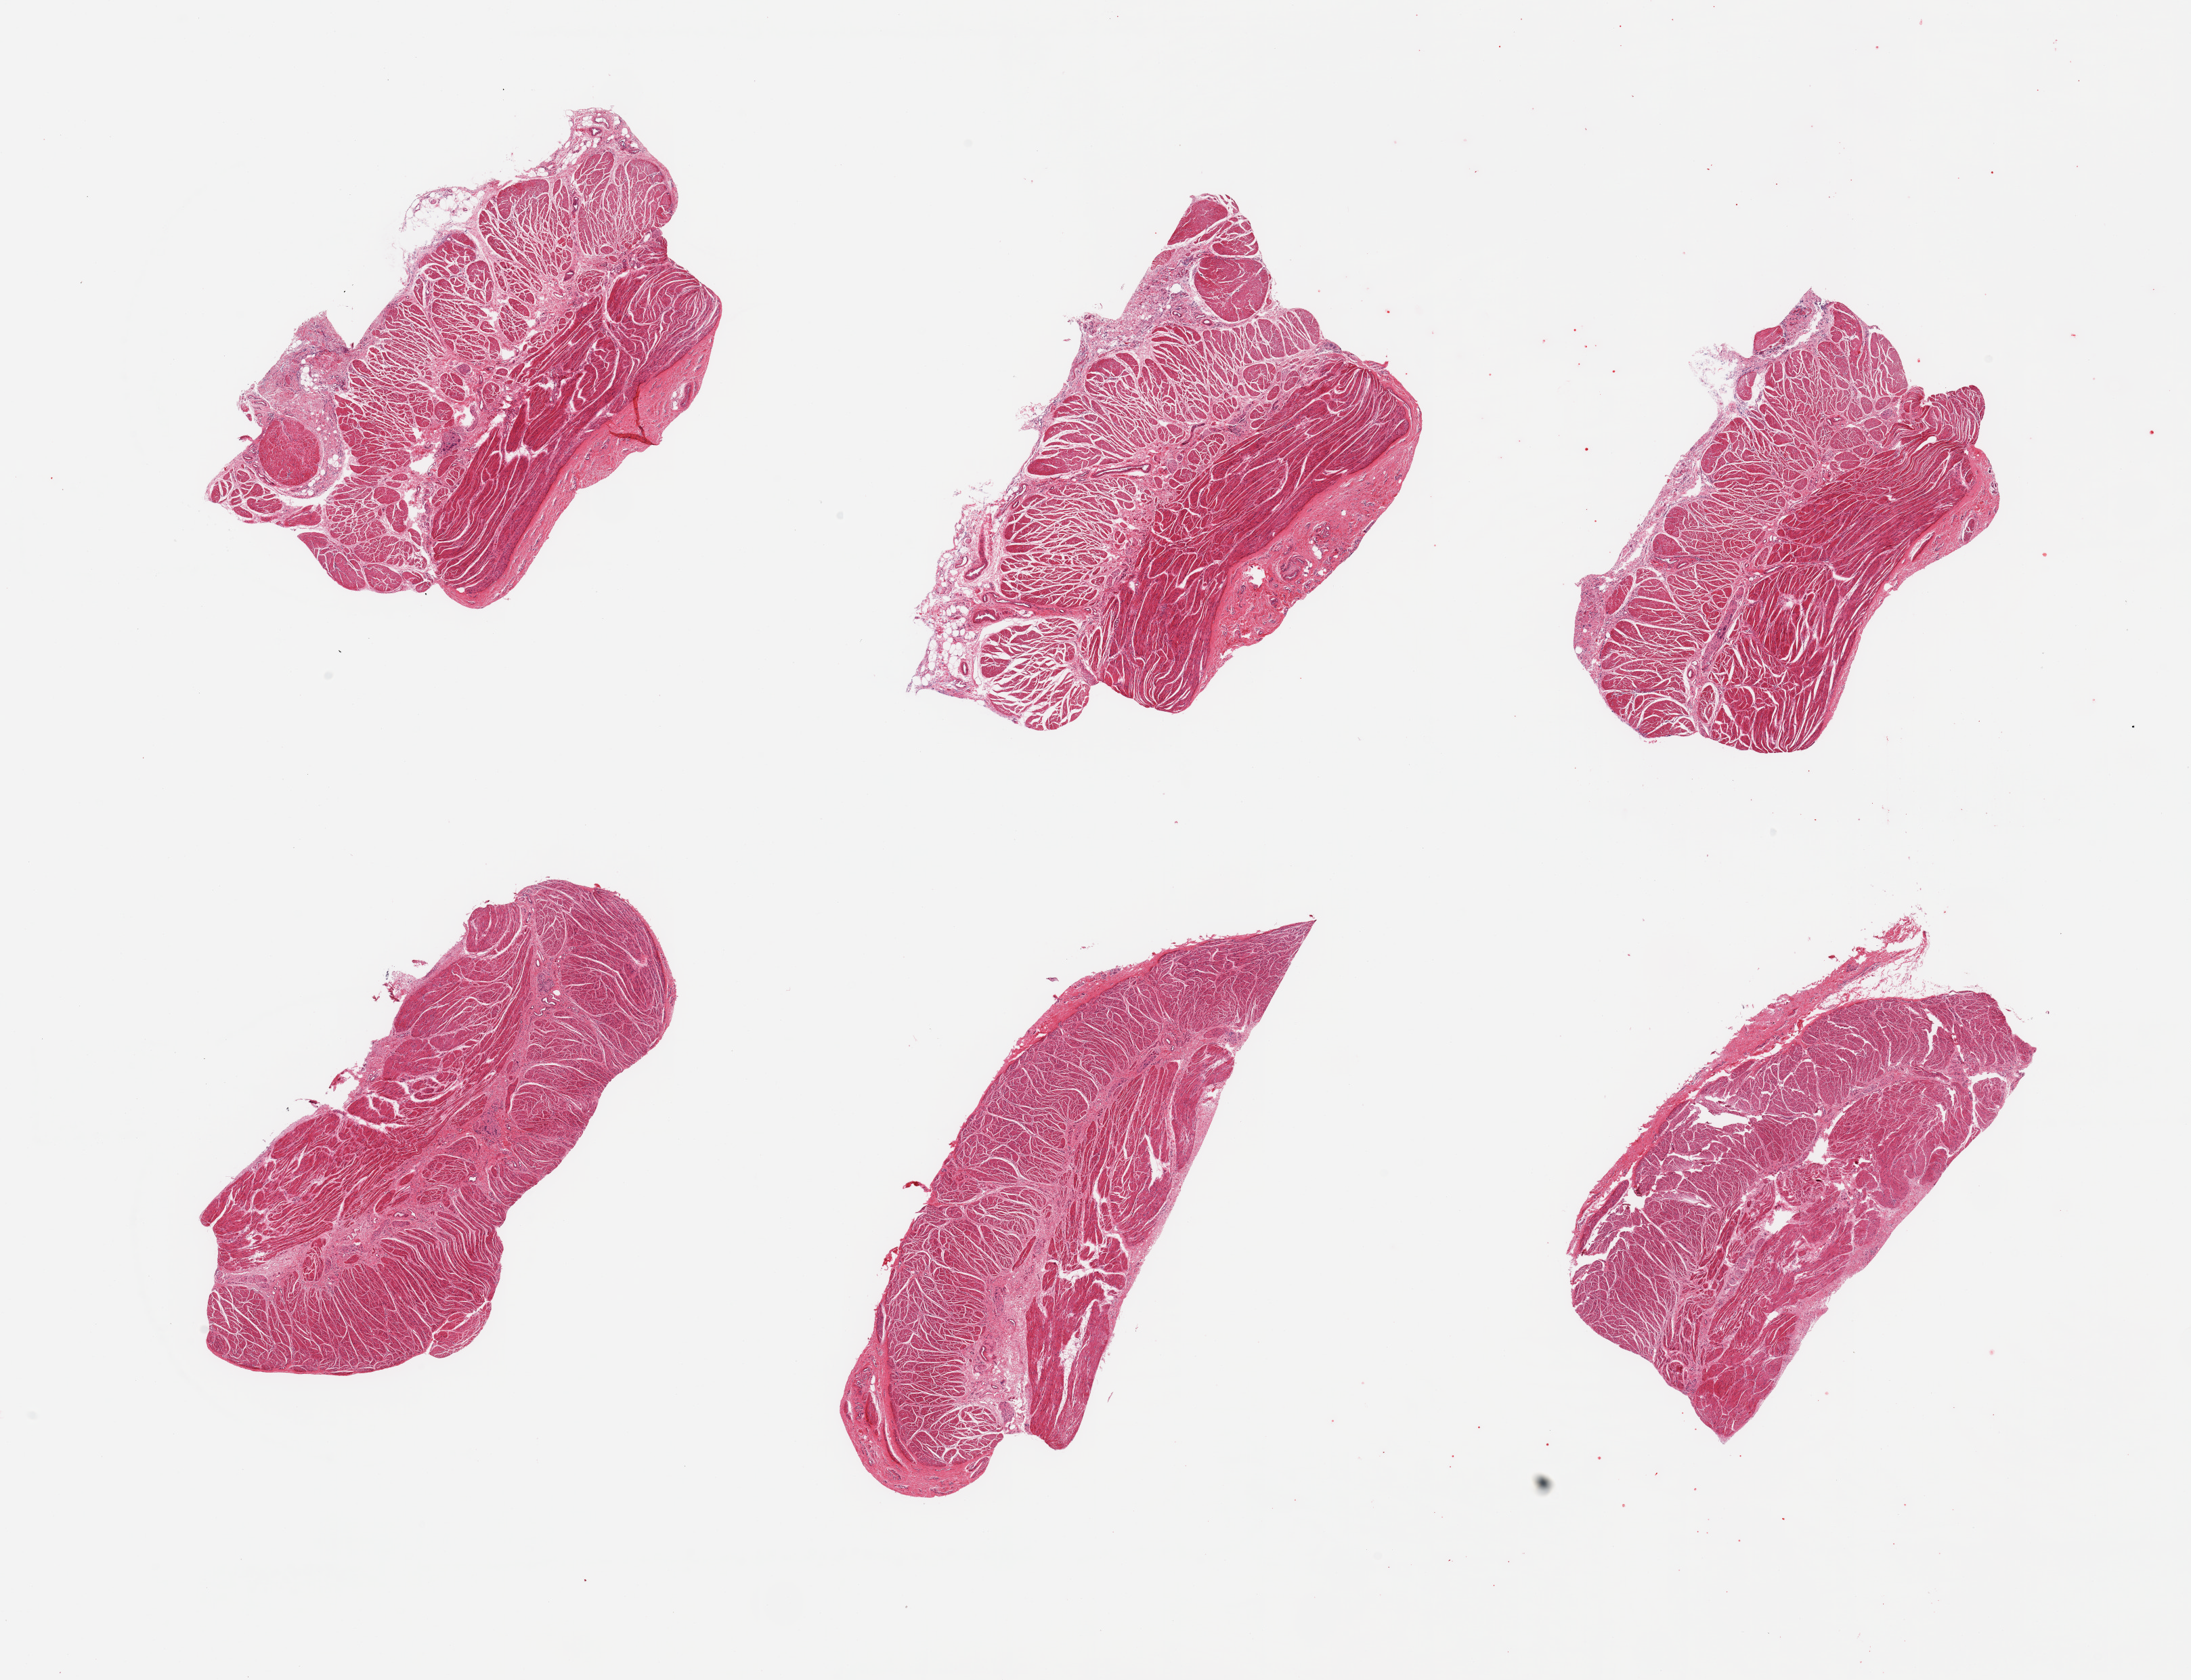
Haematoxylin and eosin whole-slide image, brightfield — whole scanned area (about 25.6 x 19.6 mm, acquisition: 20x scan) shown as a low-resolution overview, PAXgene-fixed, paraffin-embedded tissue, sampled site (target tissue): gastroesophageal junction, donor tissue sample. Donor: male.
Review note (as recorded): 6 pieces; target muscularis.